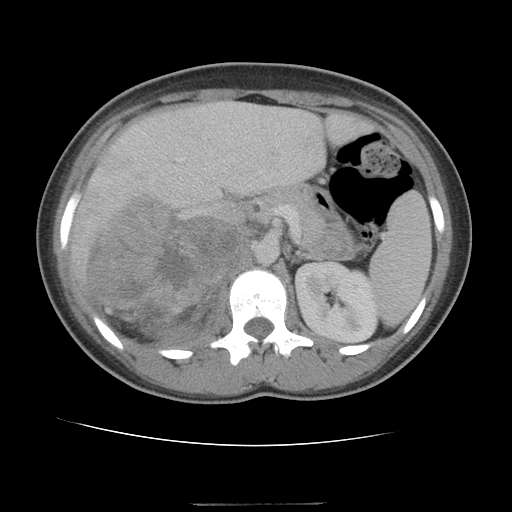
Contrast-enhanced abdominal CT, one axial slice; slice 69 of 100 in the series (ordered by position); reconstruction kernel STANDARD; 120 kVp; intravenous contrast given; soft-tissue window (W 400 / L 40 HU); 512 × 512 image matrix, field of view 360 × 360 mm. Female patient, age 21 years. Case-level facts recorded for this patient, not image findings: diagnosis: adrenocortical carcinoma; tumour side: right adrenal; tumour size at pathology: 15.5 cm; Ki-67 index: 26 %; stage (as recorded): 3.
Outlined on this slice (semi-automatic segmentation, software-assisted and operator-edited):
- mass: bounding box <89,198,237,337> (left, top, right, bottom; pixels)